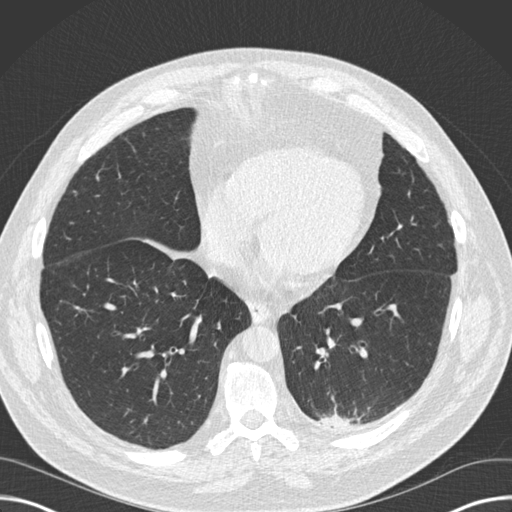
Low-dose screening chest CT, one axial slice; 120 kVp; lung window (W 1500 / L -600 HU); 512 × 512 image matrix, field of view 382 × 382 mm.
Outlined on this slice (manually delineated by an expert):
- lesion 1 (tumor, upper lobe of left lung): box from (x=319, y=414) to (x=351, y=427) px